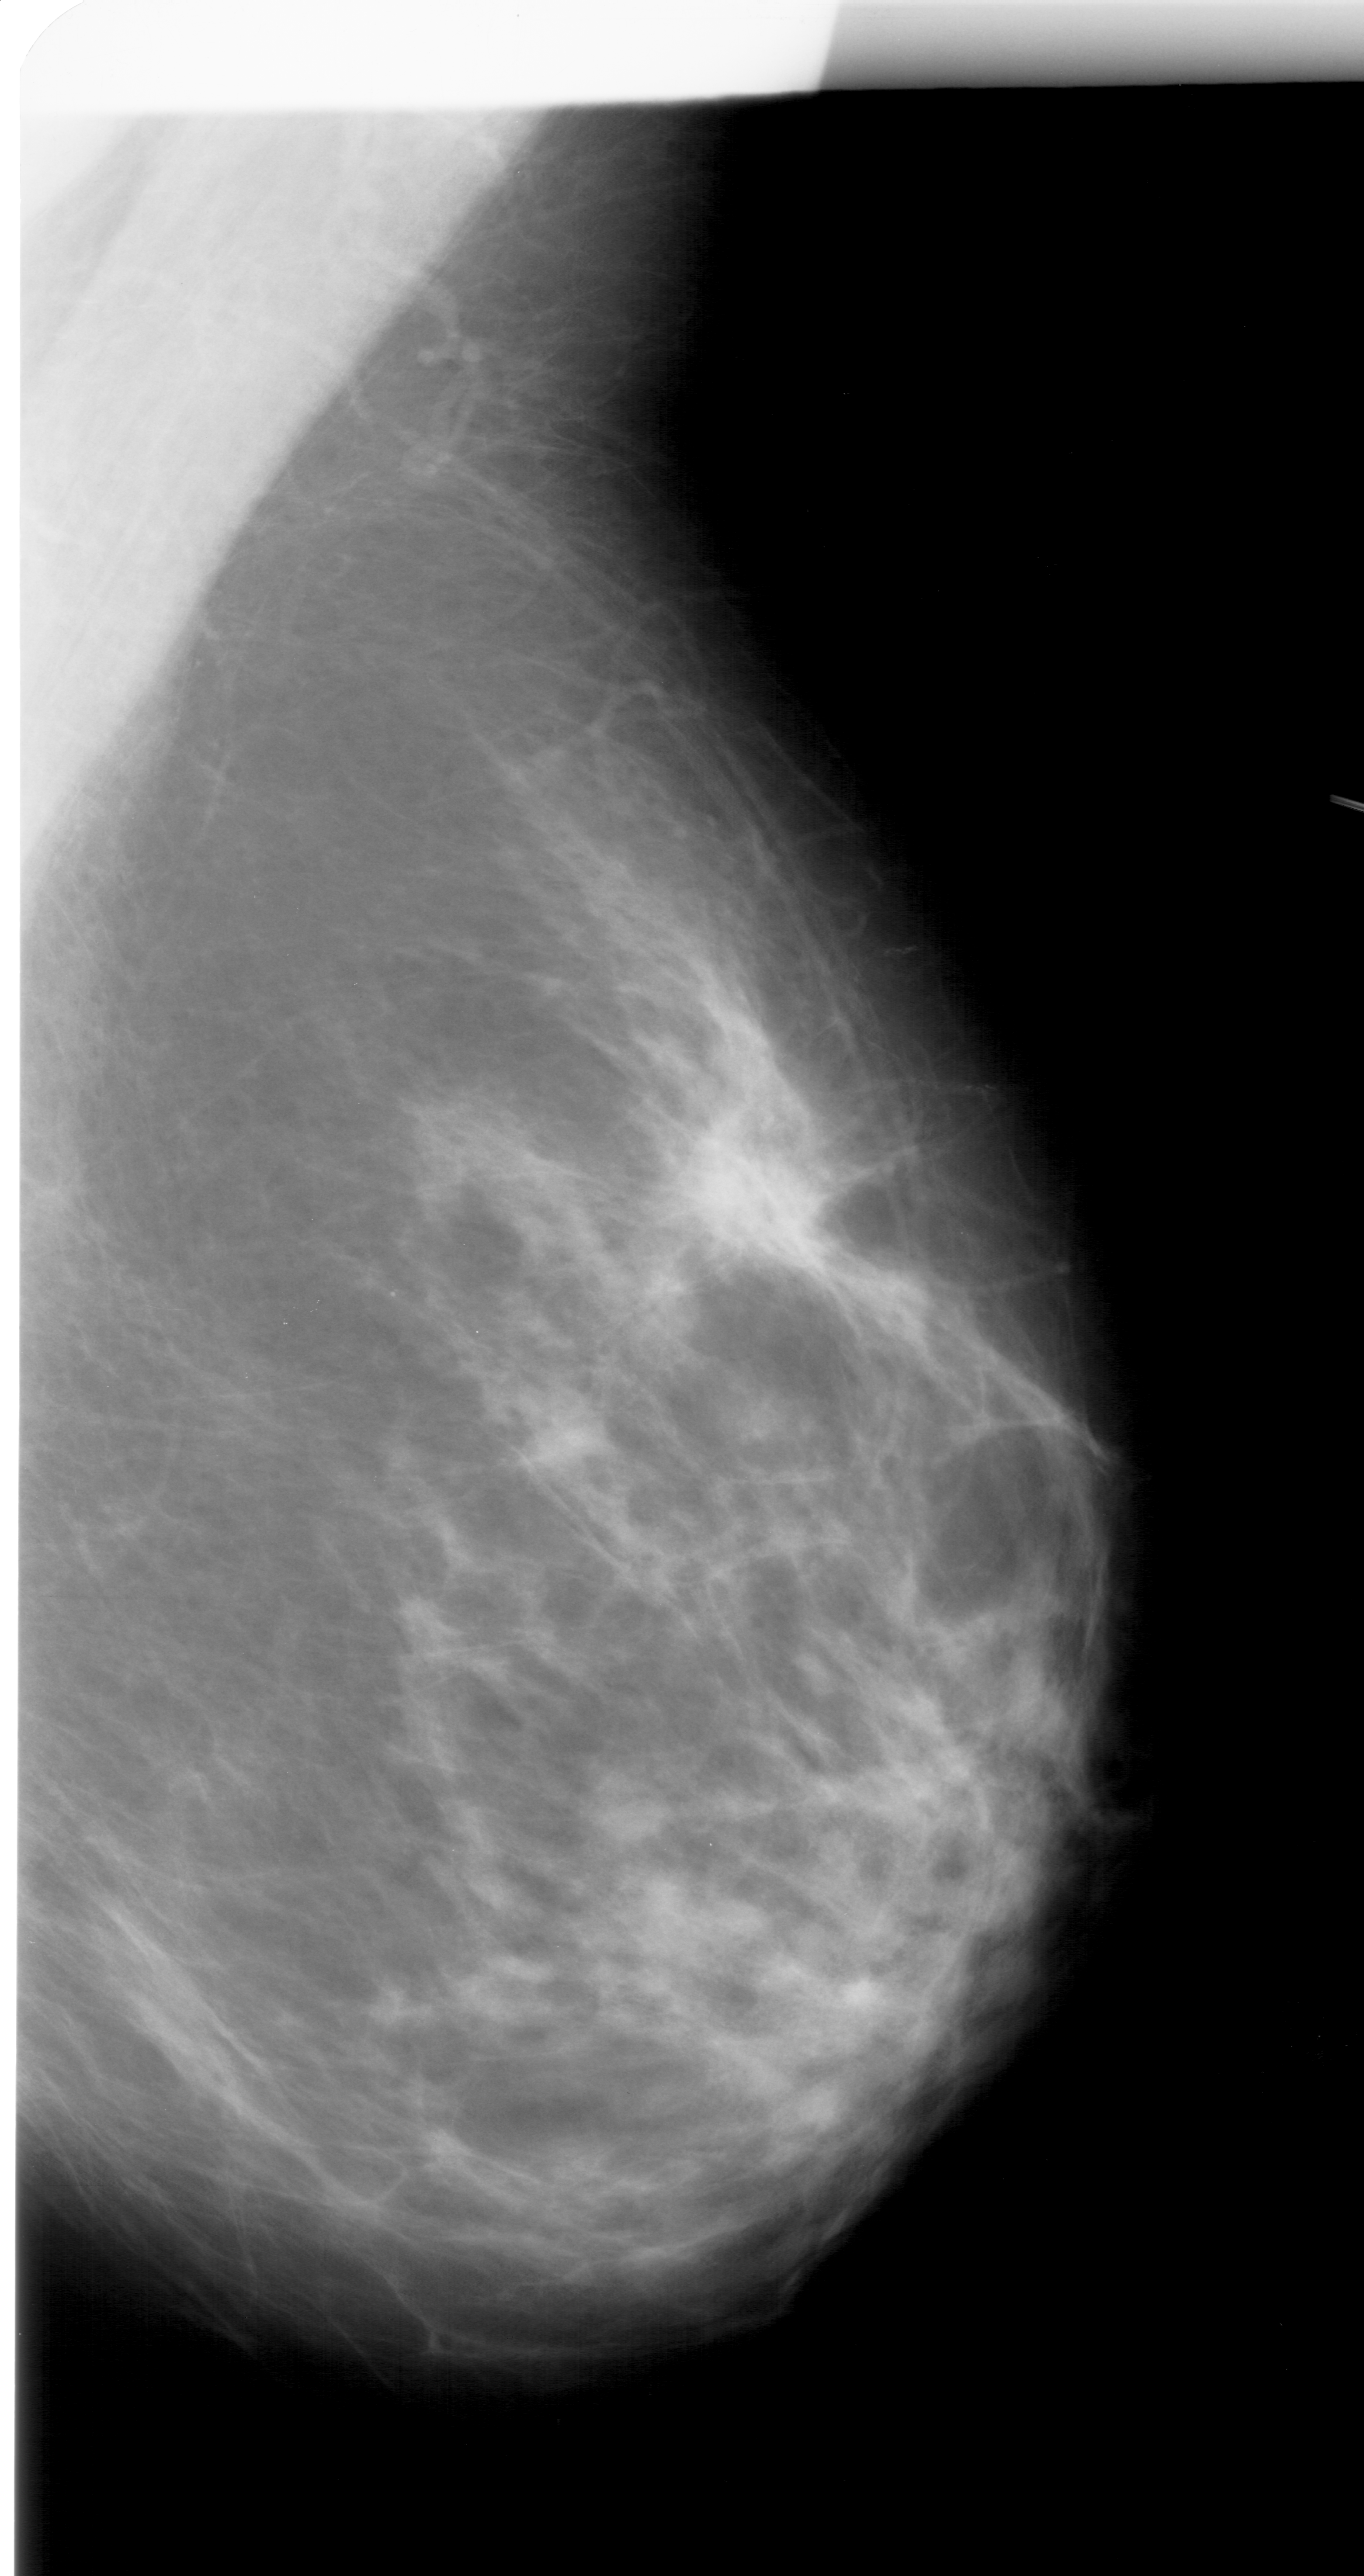
Scanned film-screen mammogram; right breast; MLO view; breast composition: heterogeneously dense (BI-RADS density category 3 of 4).
Finding: calcifications, morphology pleomorphic, distribution linear; BI-RADS assessment category 4; pathology (as recorded): benign.